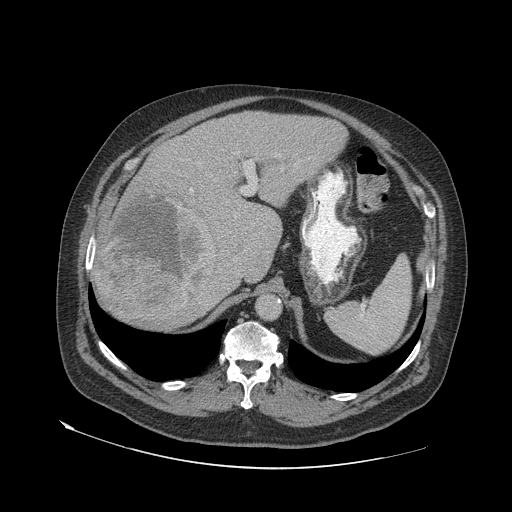
Contrast-enhanced abdominal CT (liver protocol), one axial slice. Slice 47 of 79 in the series (ordered by position). Reconstruction kernel STANDARD. 140 kVp. Soft-tissue window (W 400 / L 40 HU). 2.5 mm slice thickness. 512 × 512 image matrix, field of view 480 × 480 mm. Case-level facts recorded for this patient, not image findings: diagnosis: hepatocellular carcinoma (patient treated with transarterial chemoembolisation; whether this scan precedes or follows treatment is not stated here); TNM stage (as recorded): Stage-IVA; Child-Pugh class: A; tumour differentiation: well differentiated; tumour nodularity: multinodular.
Outlined on this slice (semi-automatically segmented with operator editing):
- liver parenchyma outside the tumour (the mass and vessels are separate outlines, so this box may not span the whole liver): bounding box <94,110,346,328> (left, top, right, bottom; pixels)
- mass: <99,194,217,322>
- liver vessels: <190,161,251,192>